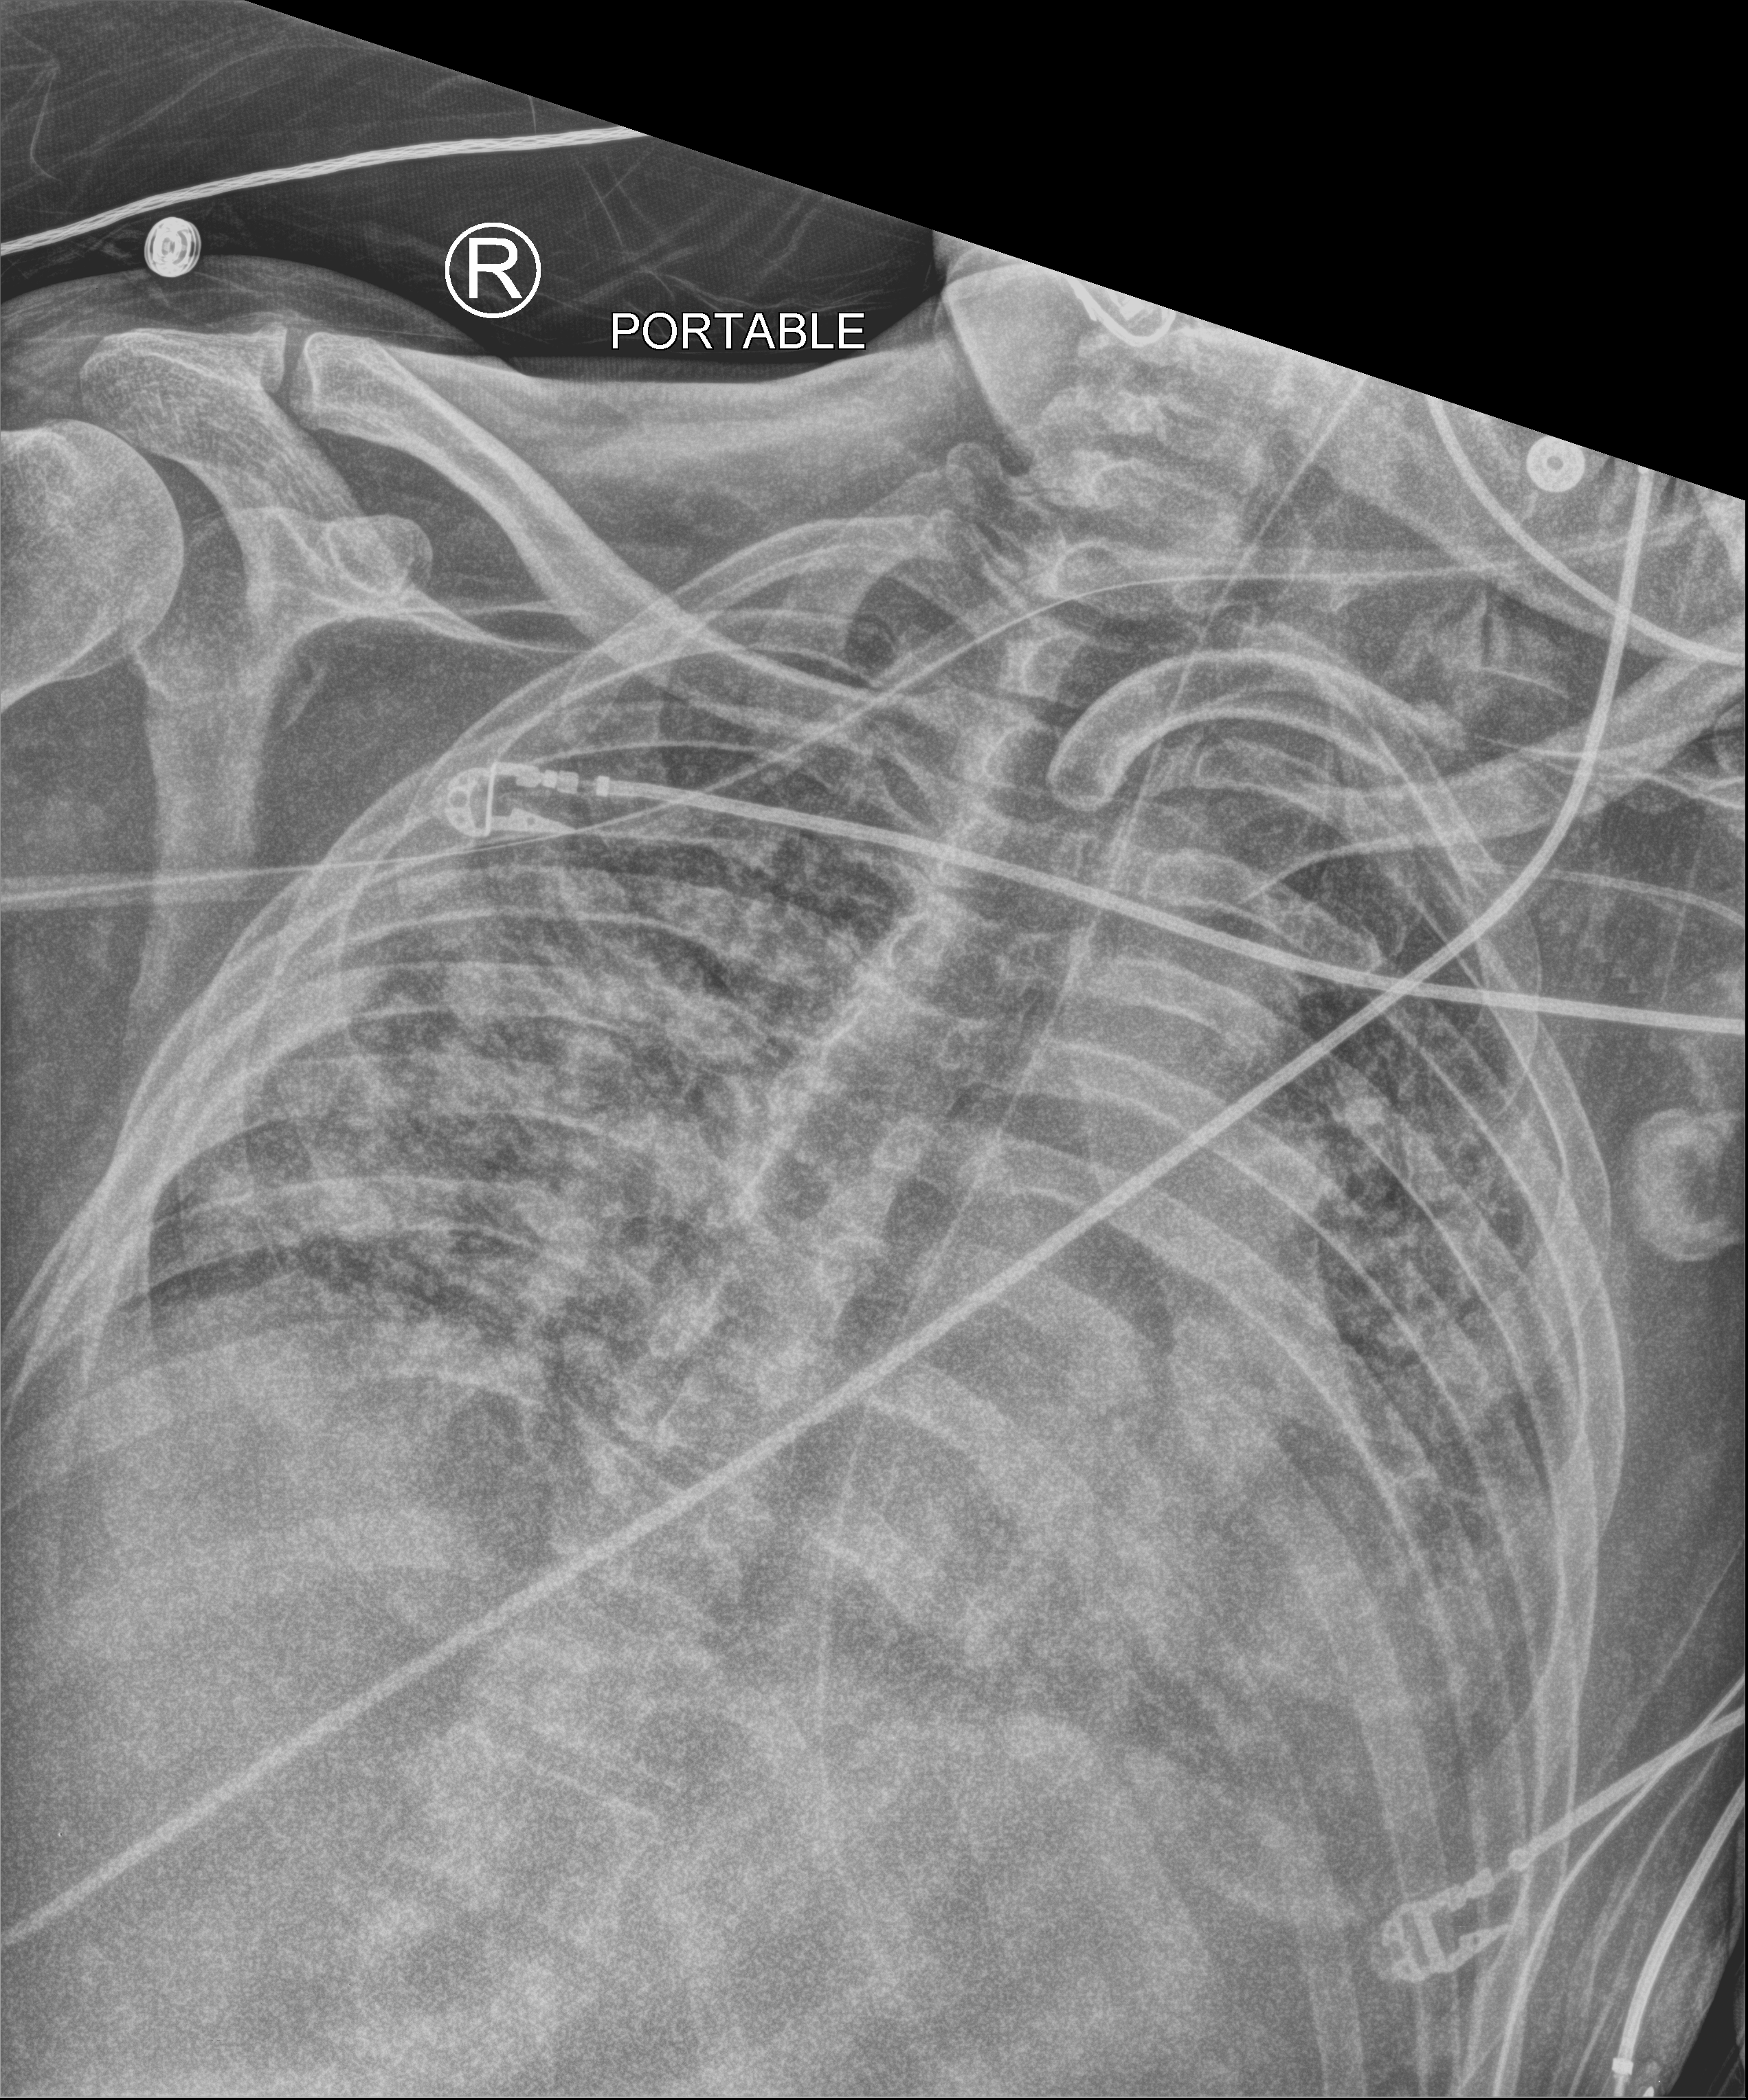
Portable chest radiograph, anteroposterior (AP) projection. Male patient hospitalised with COVID-19, age 18–59 years.
Hospital-stay facts (about this admission, not read from this image; timing relative to this image not recorded):
- length of hospital stay: 75 days